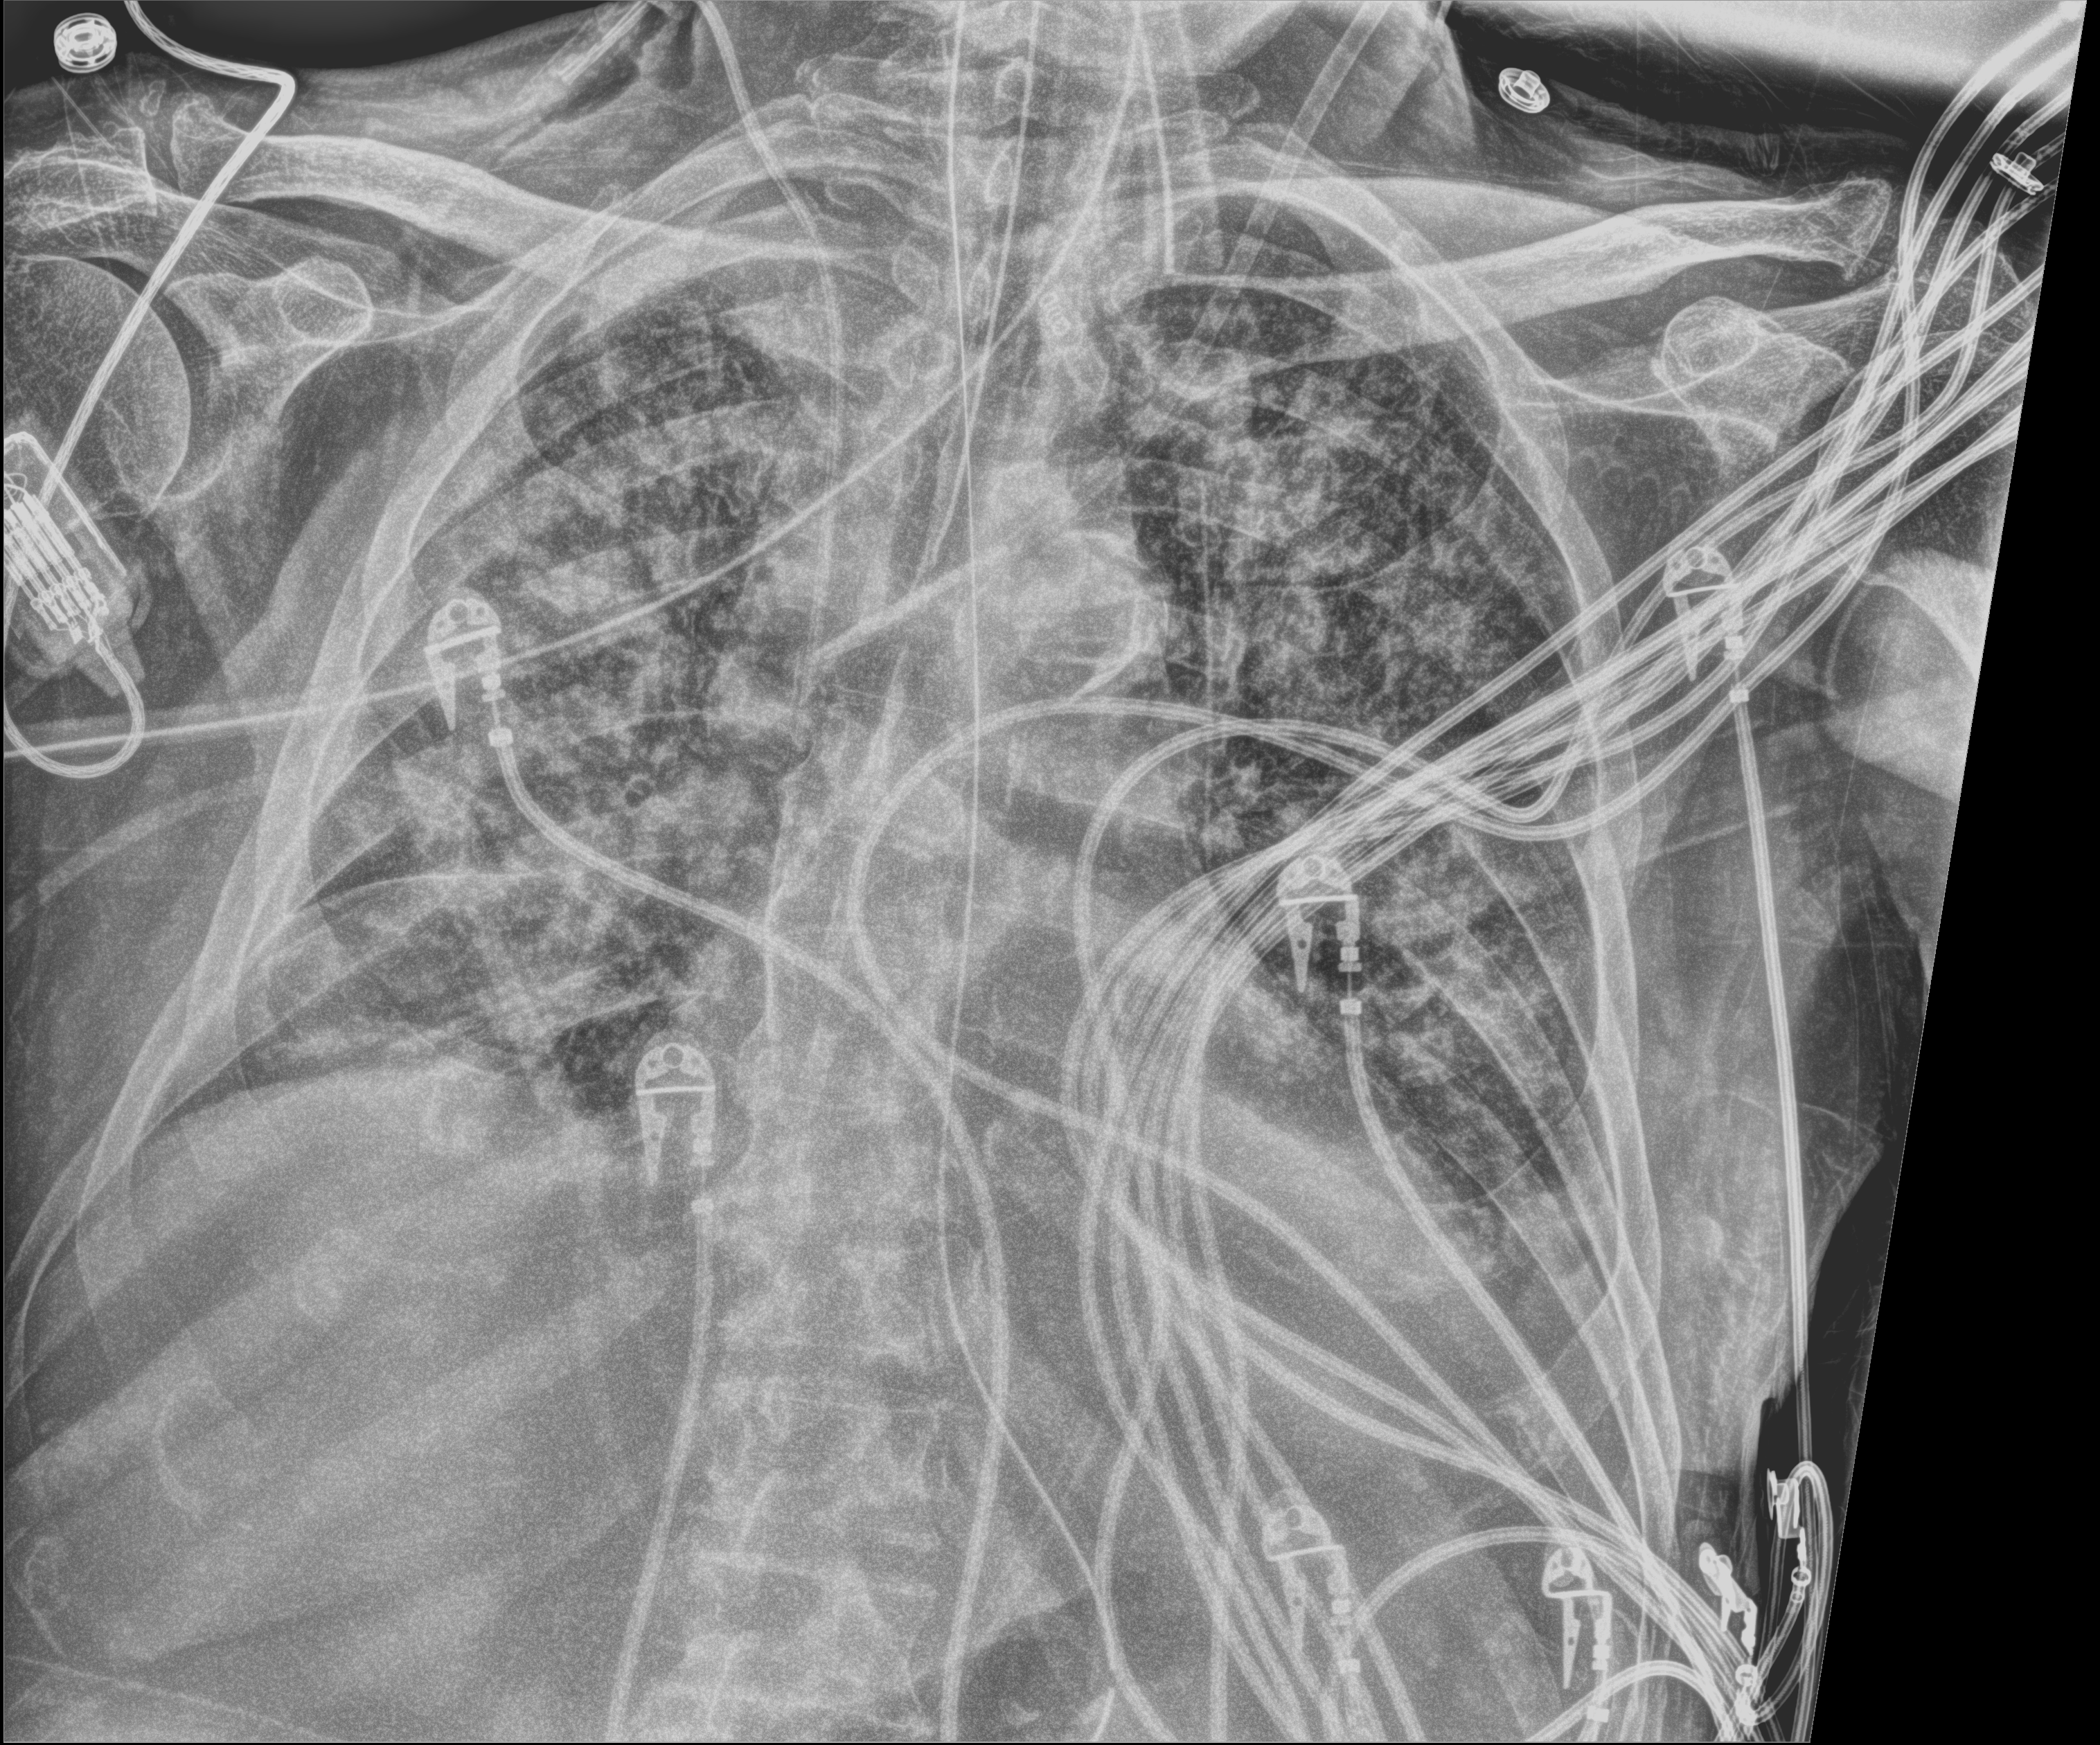
Portable chest radiograph, anteroposterior (AP) projection. Patient hospitalised with COVID-19; male, aged 75–90 years.
Hospital-stay facts (about this admission, not read from this image; timing relative to this image not recorded):
- admitted to intensive care during this hospital stay: yes
- other chronic lung disease (admission record): no
- mechanically ventilated during this hospital stay: yes